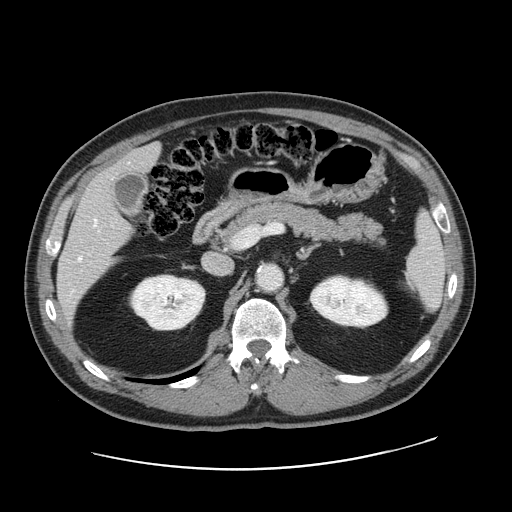
Contrast-enhanced abdominal CT, one axial slice. Position 88 of 178 along the scan axis. 120 kVp. Intravenous contrast given. Soft-tissue window (W 400 / L 40 HU). 2.5 mm slice thickness. 512 × 512 image matrix. Male patient, age 63 years. Case-level facts recorded for this patient, not image findings: diagnosis: colorectal cancer liver metastases, imaged before liver resection; multiple liver metastases: yes; largest metastasis: 8 cm; disease in both lobes: yes.
Structures marked on this image (expert manual segmentation):
- hepatic veins: bounding box (x1, y1, x2, y2) in pixels: (78, 219, 97, 260)
- liver: (58, 146, 159, 315)
- planned liver remnant (the part of the liver to remain after resection): (114, 146, 159, 173)